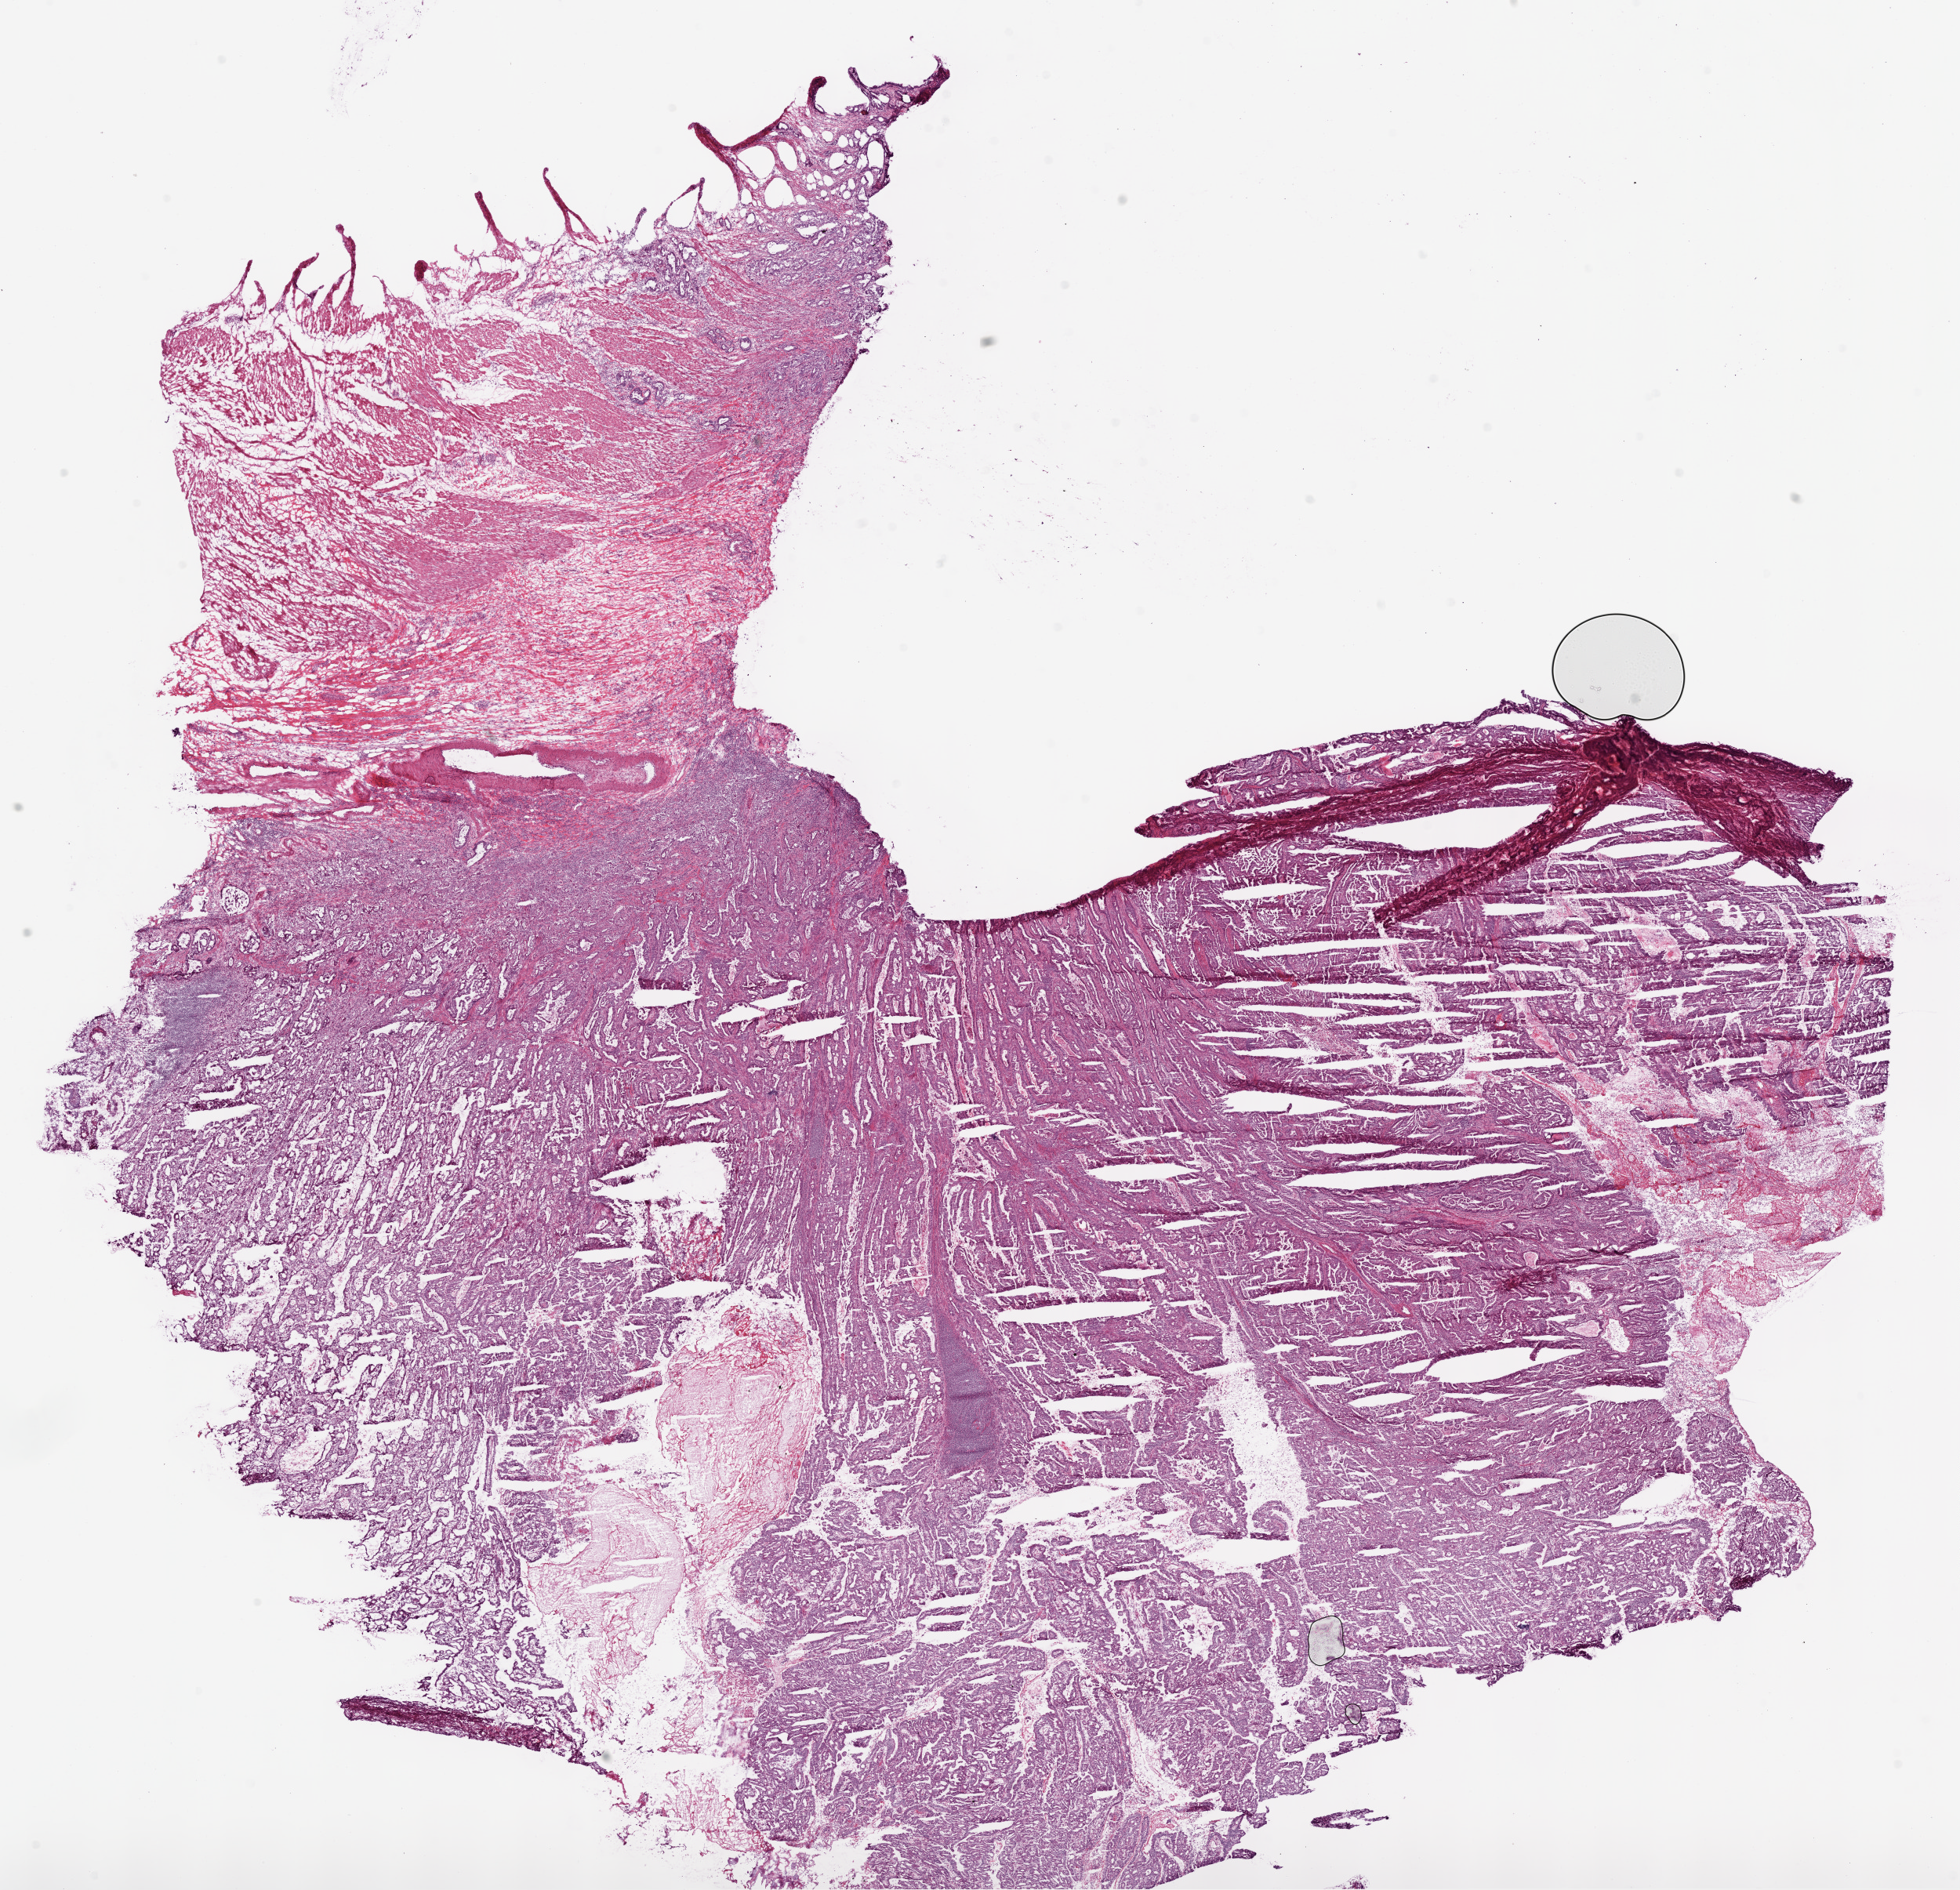
H&E whole-slide image — a low-resolution overview of the entire scanned area, about 20.1 x 19.3 mm. Frozen section from the top of the tissue portion. Primary tumour sample from the stomach. Male patient; age at initial diagnosis 51 years. Histologic grade: G2 (moderately differentiated). Pathologist review of this section (percent, as recorded): tumour cells 95%, tumour nuclei 85%, normal cells 0%, stromal cells 3%, necrosis 2%.
AJCC pathologic stage: IB (6th edition). Diagnosis: Adenocarcinoma, NOS (body of stomach). TNM: T2a N0 M0.